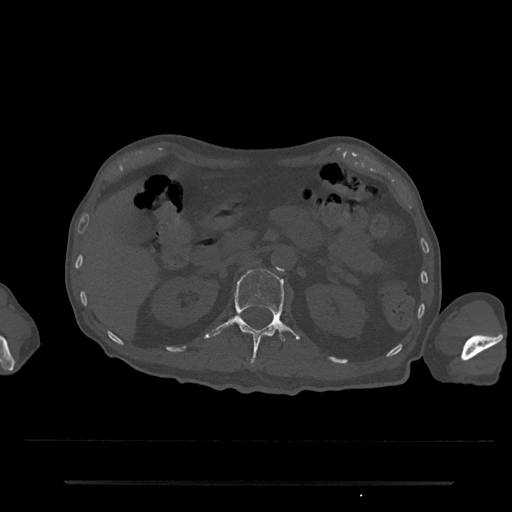
CT including the spine, one axial slice. Position 128 of 797 along the scan axis. Bone window (W 1800 / L 400 HU). 512 × 512 image matrix, field of view 427 × 427 mm. Patient: male, 74 years. Case-level facts recorded for this patient, not image findings: primary cancer: prostate.
Outlined on this slice (semi-automatically segmented with operator editing):
- L1 vertebra: bounding box [x1, y1, x2, y2] px = [204, 269, 301, 358]